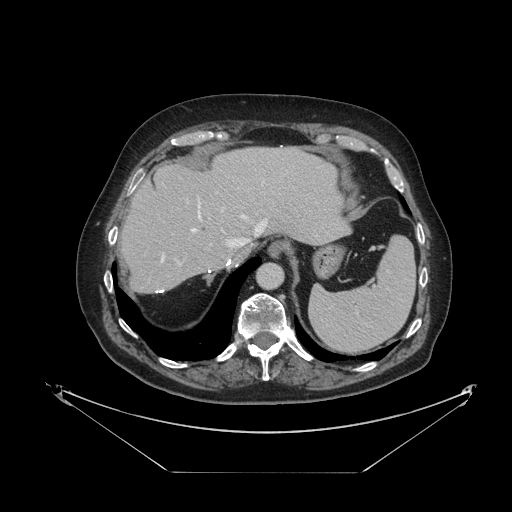
Contrast-enhanced abdominal CT, one axial slice; 120 kVp; intravenous contrast given; soft-tissue window (W 400 / L 40 HU); 2.5 mm slice thickness; 512 × 512 image matrix. Male patient, age 68 years. Case-level facts recorded for this patient, not image findings: diagnosis: colorectal cancer liver metastases, imaged before liver resection; multiple liver metastases: no; largest metastasis: 4 cm; disease in both lobes: no.
Structures marked on this image (expert manual segmentation):
- hepatic veins: bounding box (x1, y1, x2, y2) in pixels: (161, 181, 267, 261)
- liver: (121, 148, 348, 293)
- planned liver remnant (the part of the liver to remain after resection): (121, 148, 348, 293)
- portal vein (with intrahepatic branches): (177, 208, 224, 266)